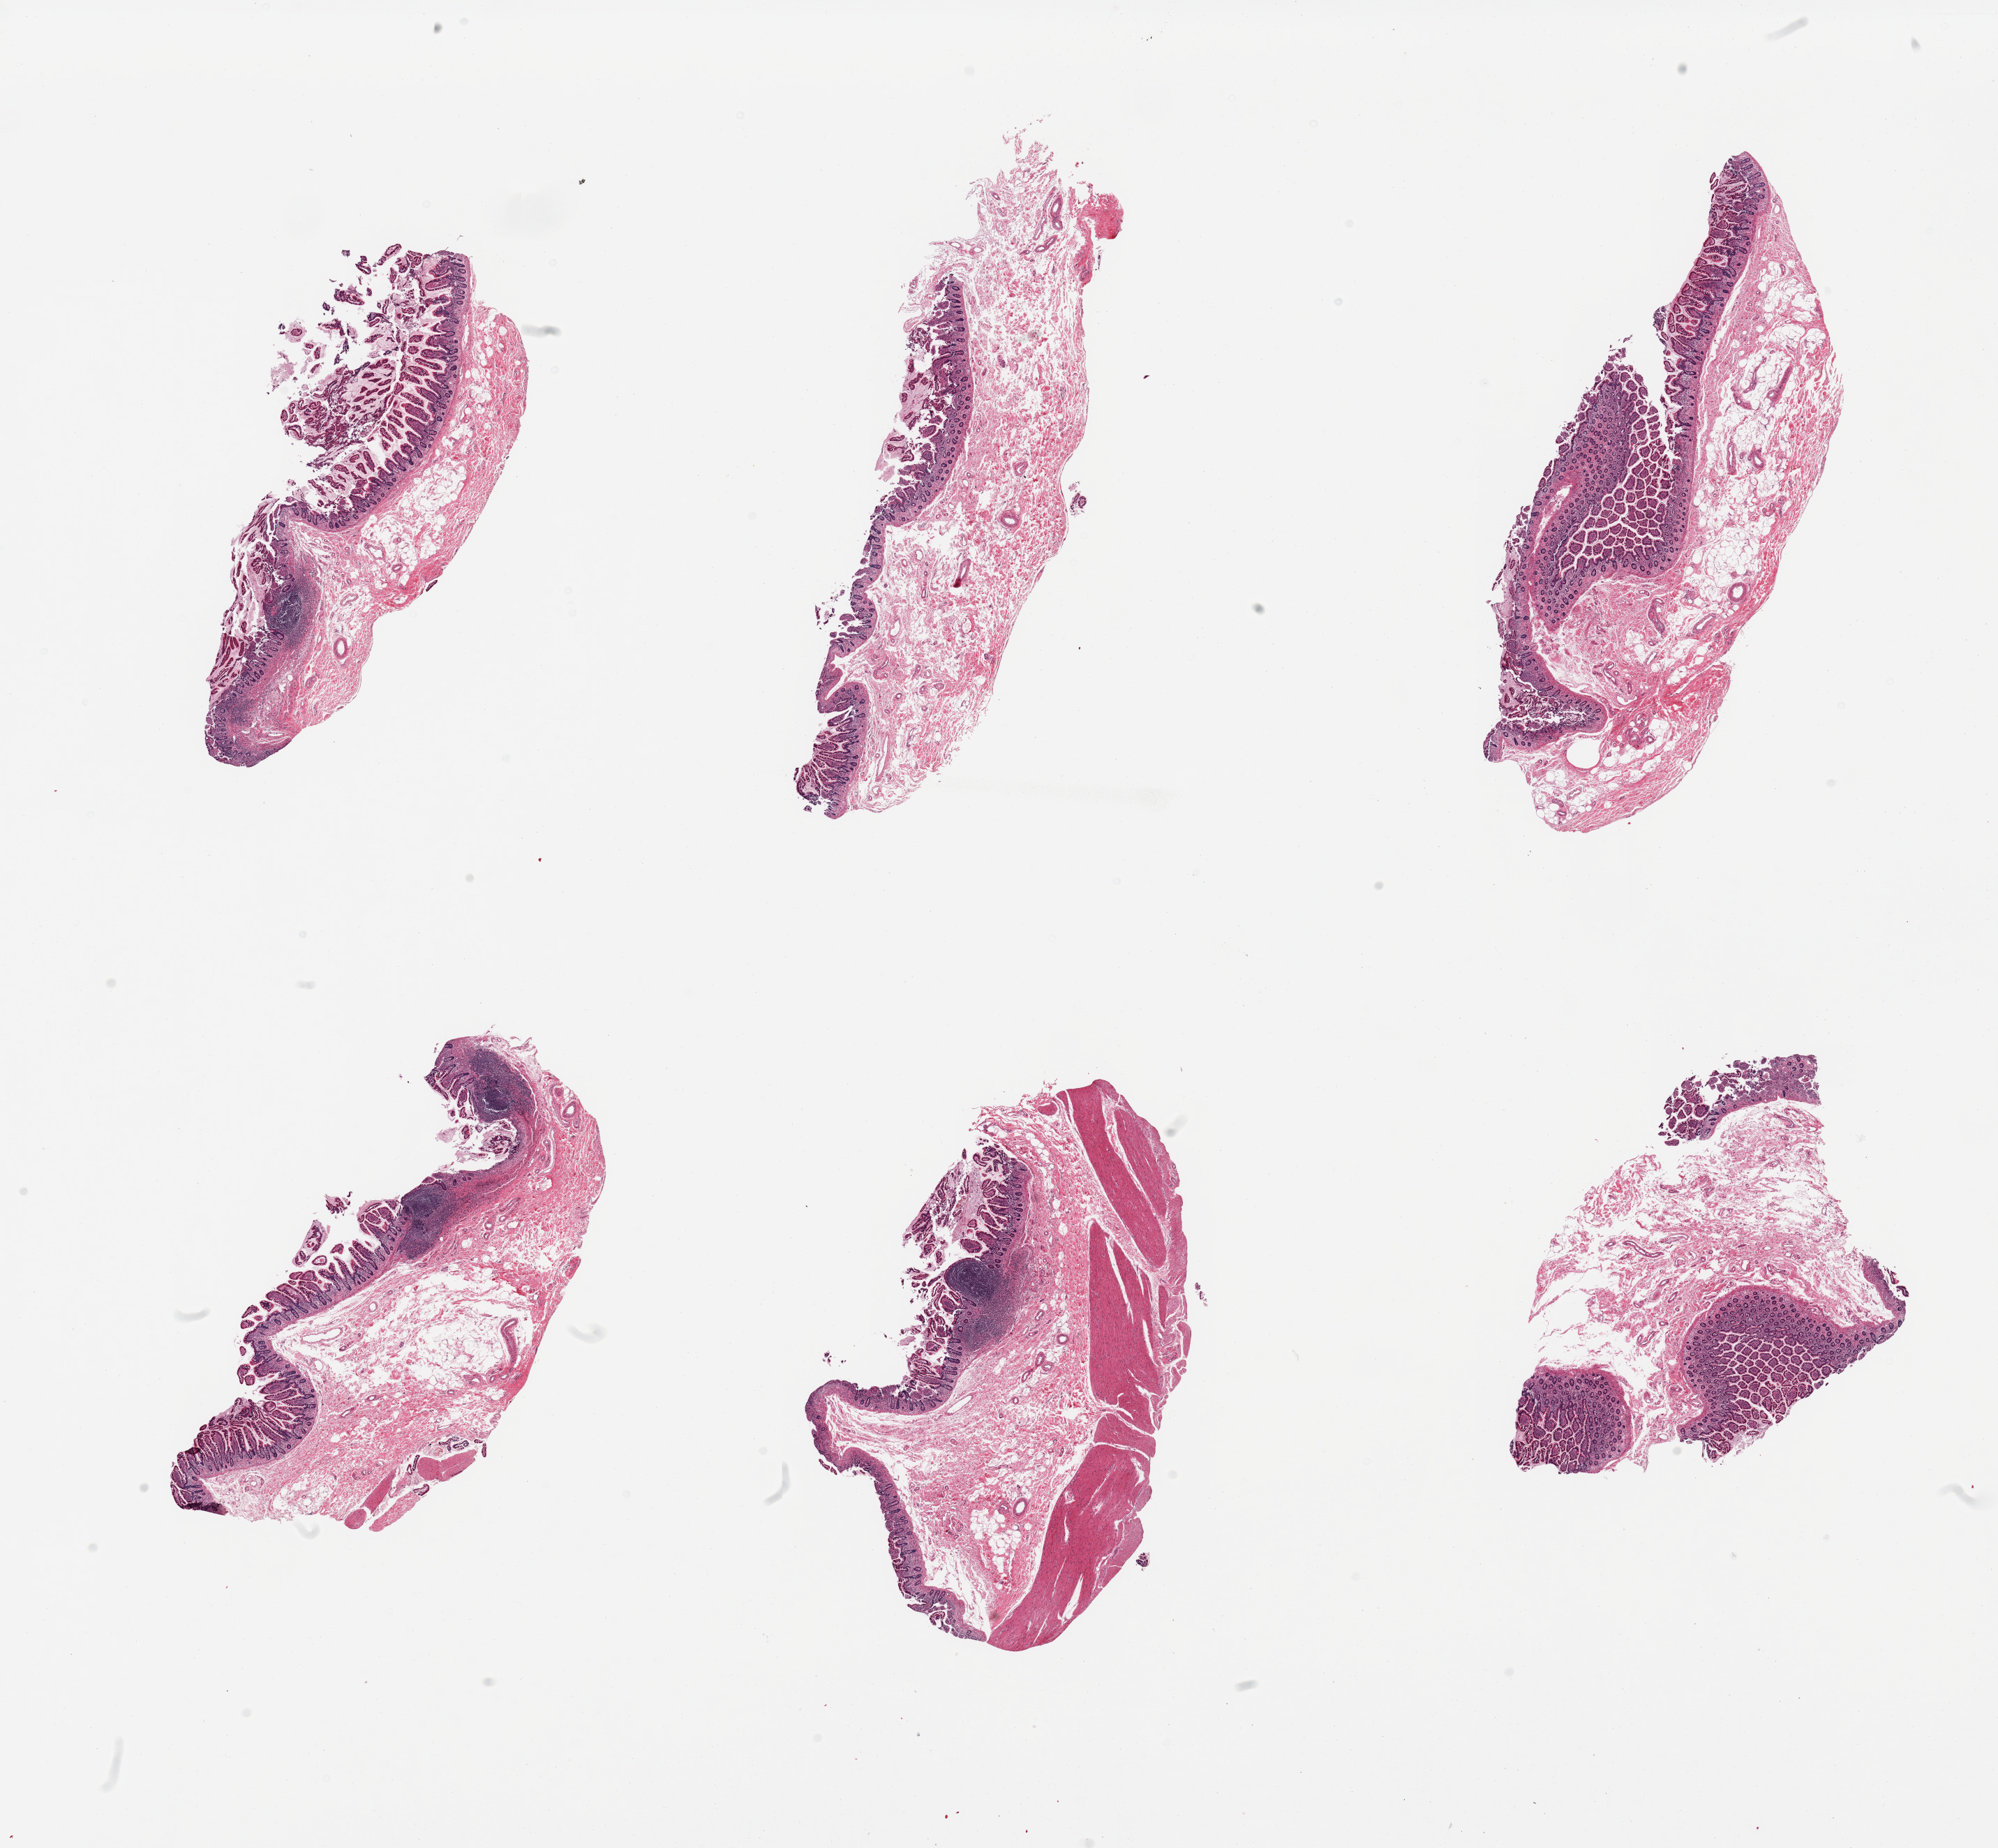
Whole-slide image, H&E stain — whole scanned area (about 22.6 x 20.9 mm, from a 20x scan) shown as a low-resolution overview; PAXgene-fixed paraffin-embedded (PFPE) section; section of ileum (target tissue); tissue donor sample. Male donor.
Reviewer comment on this tissue sample: 6 pieces; scattered lymphoid aggregates, mucosa focally mildly autolyzed, one piece includes muscularis.